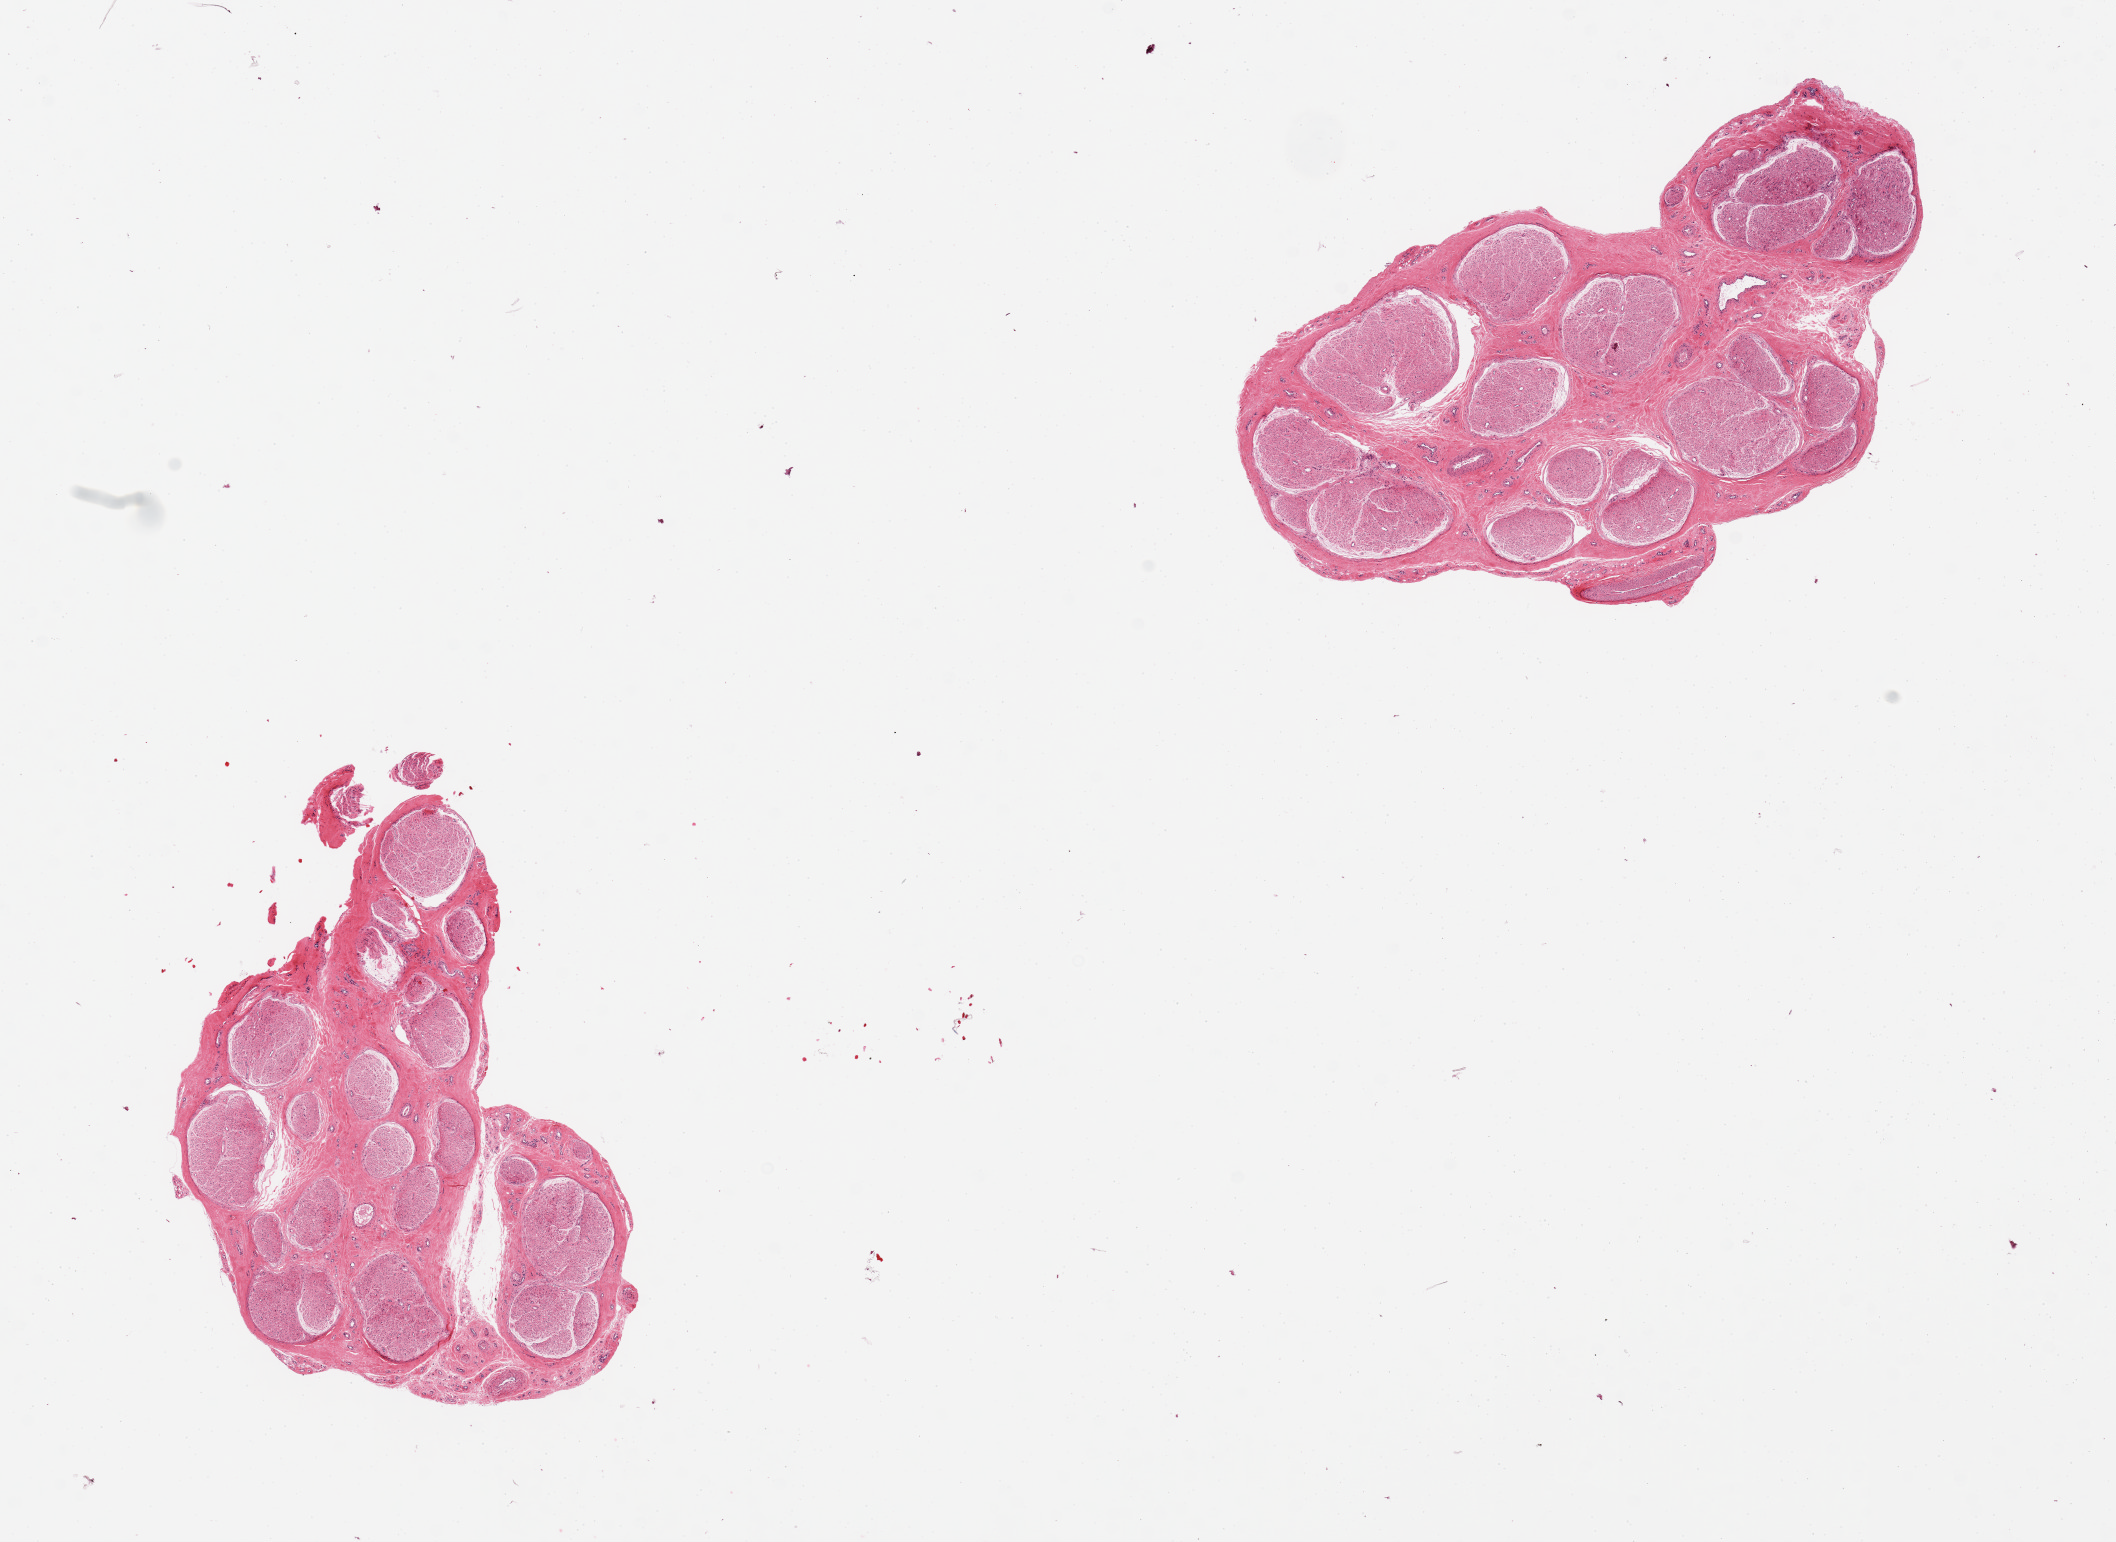
Digitized H&E-stained section, brightfield, shown as a low-resolution overview of the whole scanned area (about 16.7 x 12.2 mm, slide scanned at 20x); PAXgene-fixed, paraffin-embedded tissue; sampled site (target tissue): tibial nerve; tissue donor sample. Male donor.
• reviewer comment on this tissue sample: 2 pieces, good clean specimens, minimal fat